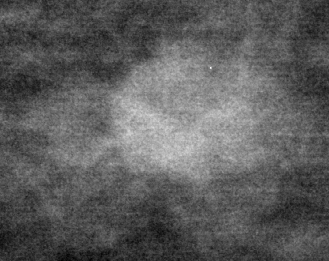
Crop from a digitized film mammogram around one marked abnormality; right breast; CC view.
Finding: mass, shape oval, margins circumscribed; BI-RADS assessment category 3; subtlety rating 5 on a 1 (subtle) to 5 (obvious) scale; pathology result (as recorded, not read from the image): benign.